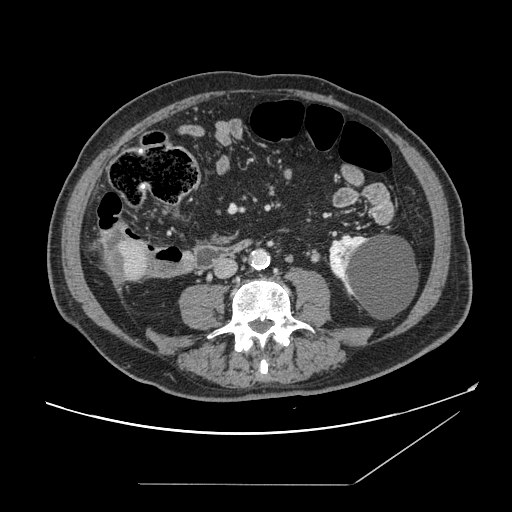
Contrast-enhanced abdominal CT, one axial slice; position 25 of 166 along the scan axis; 120 kVp; intravenous contrast given; soft-tissue window (W 400 / L 40 HU); 2.5 mm slice thickness; 512 × 512 image matrix, field of view 416 × 416 mm. Male patient, age 80 years. Case-level facts recorded for this patient, not image findings: diagnosis: colorectal cancer liver metastases, imaged before liver resection; multiple liver metastases: no; largest metastasis: 2.2 cm; disease in both lobes: no.
Outlined on this slice (manually delineated by an expert):
- liver: box from (x=102, y=232) to (x=150, y=284) px
- liver metastasis: (x=105, y=237)–(x=128, y=282)